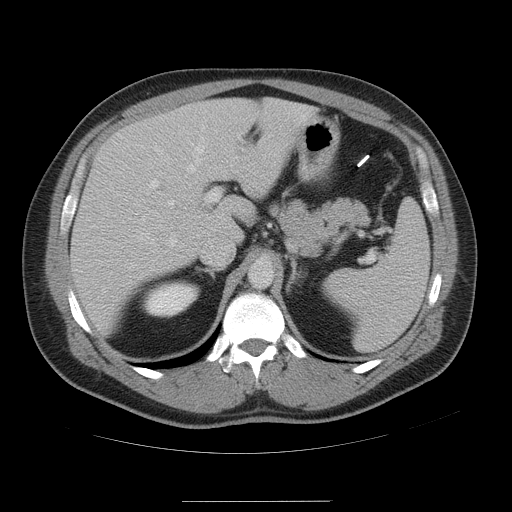
Contrast-enhanced abdominal CT, one axial slice. Position 33 of 54 along the scan axis. 120 kVp. Intravenous contrast given. Soft-tissue window (W 400 / L 40 HU). 5 mm slice thickness. 512 × 512 image matrix. Male patient, age 40 years. From the clinical record (not read from this slice): diagnosis: colorectal cancer liver metastases, imaged before liver resection; multiple liver metastases: no; largest metastasis: 15 cm; disease in both lobes: no.
Structures marked on this image (manually delineated by an expert):
- hepatic veins: bounding box (x1, y1, x2, y2) in pixels: (140, 128, 204, 247)
- liver: (70, 97, 321, 333)
- planned liver remnant (the part of the liver to remain after resection): (194, 98, 321, 242)
- portal vein (with intrahepatic branches): (149, 180, 220, 207)